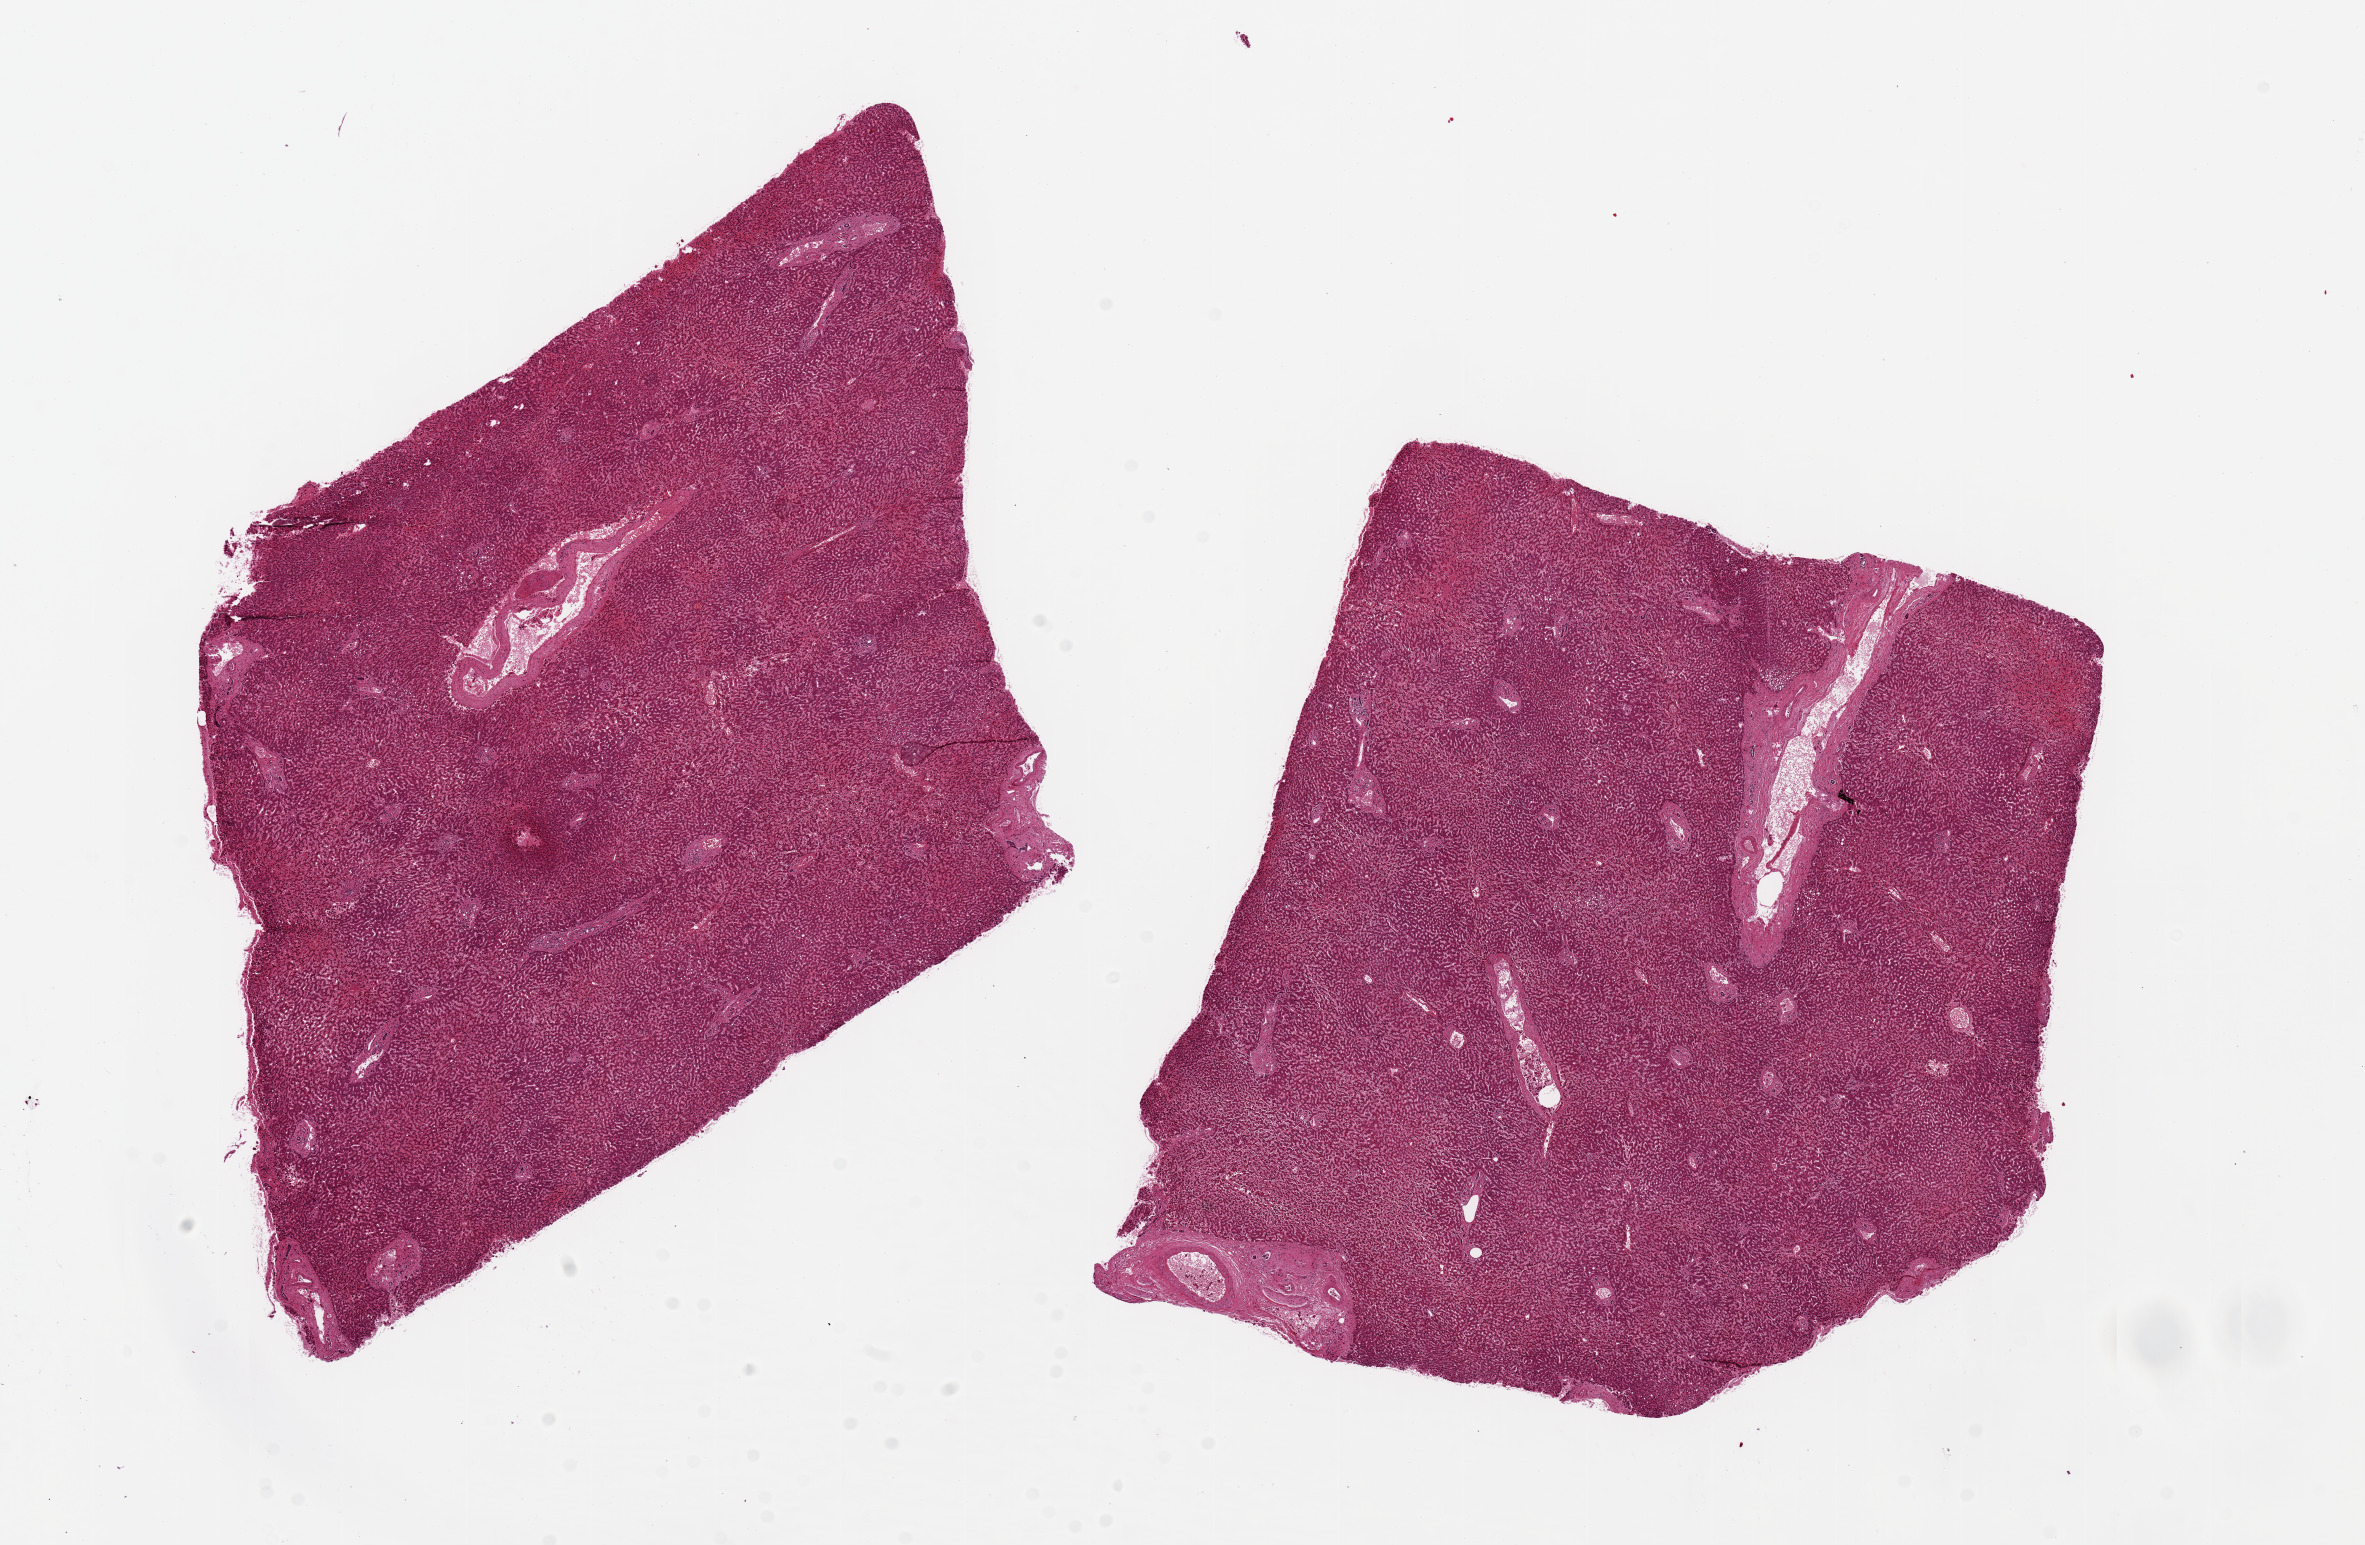
Haematoxylin and eosin whole-slide image, brightfield, whole scanned area (about 18.7 x 12.2 mm) shown as a low-resolution overview. PAXgene-fixed paraffin-embedded (PFPE) section. Section of liver (target tissue). Donor tissue sample.
* review note (as recorded): 2 pieces, up to 8x7 & 7x7mm; No fat